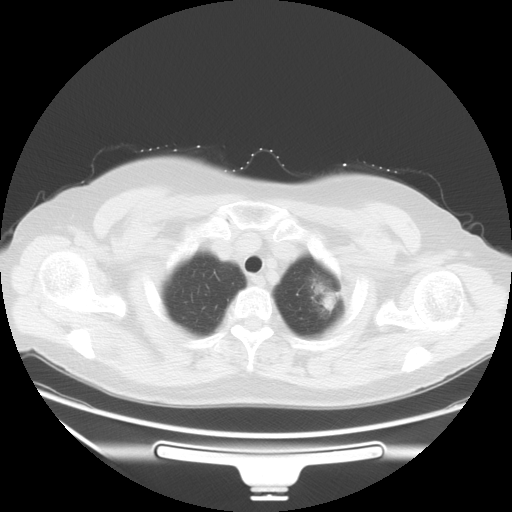
Chest CT, one axial slice; slice 49 of 53 in the series (ordered by position); reconstruction kernel STANDARD; lung window (W 1500 / L -600 HU); 5 mm slice thickness; 512 × 512 image matrix, field of view 403 × 403 mm. Patient: female, 66 years. From the clinical record (not read from this slice): clinical TNM (as recorded): T2 N0 M0; histopathological grade: G2.
Structures marked on this image (bounding box drawn by a radiologist):
- lung tumour (recorded histology: adenocarcinoma): bounding box (x1, y1, x2, y2) in pixels: (301, 264, 342, 330)